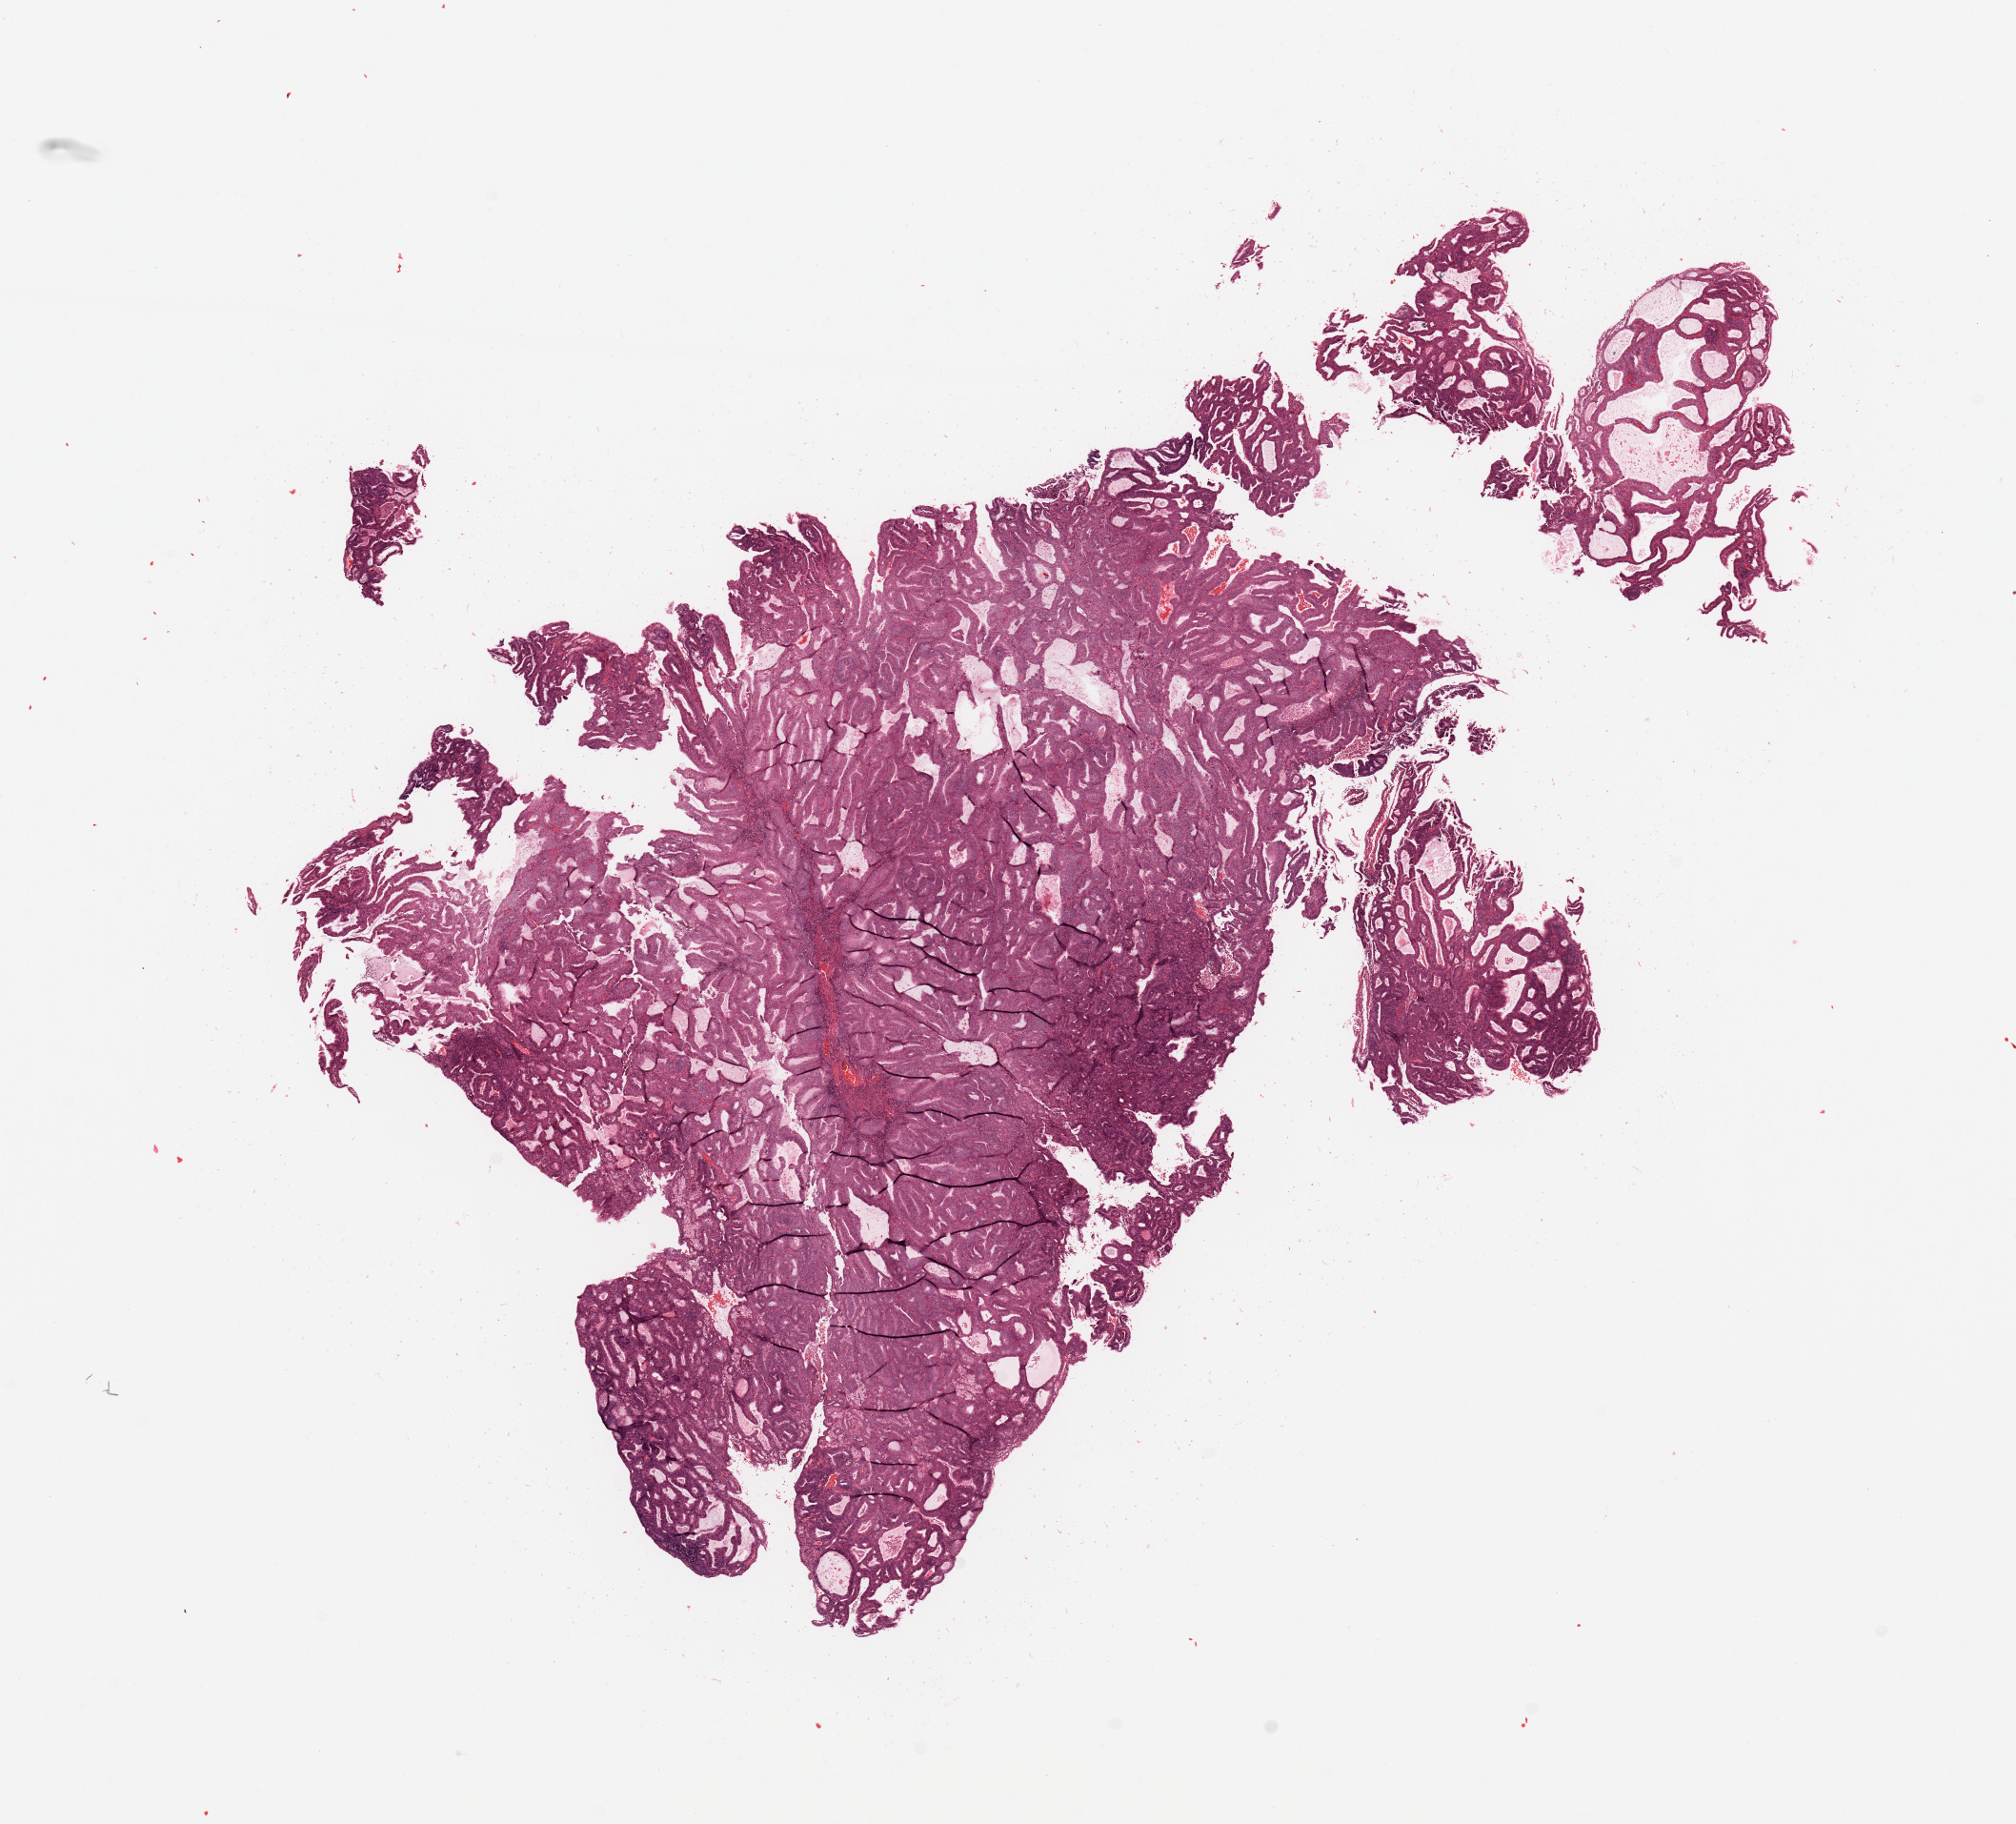
Hematoxylin and eosin (H&E) stained whole-slide image — shown as a low-resolution overview of the whole scanned area (about 16.7 x 15.1 mm, slide scanned at 20x); tumour tissue sample, sampled site: uterus. 74-year-old female patient. Histologic grade: G1 (well differentiated). Slide review estimates, as recorded: tumour nuclei 85%, necrosis 0%.
• histologic diagnosis: Endometrioid adenocarcinoma, NOS
• AJCC pathologic stage: I